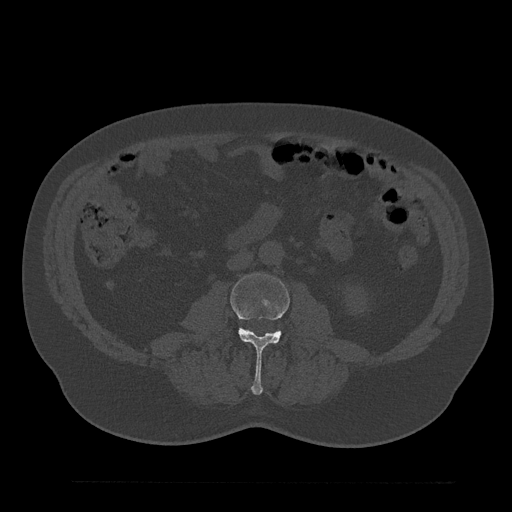
CT including the spine, one axial slice. Slice 25 of 797 in the series (ordered by position). Bone window (W 1800 / L 400 HU). 0.5 mm slice thickness. 512 × 512 image matrix. Male patient, age 61 years. From the clinical record (not read from this slice): primary cancer: prostate.
Outlined on this slice (semi-automatic segmentation, software-assisted and operator-edited):
- L3 vertebra: box from (x=230, y=273) to (x=289, y=394) px